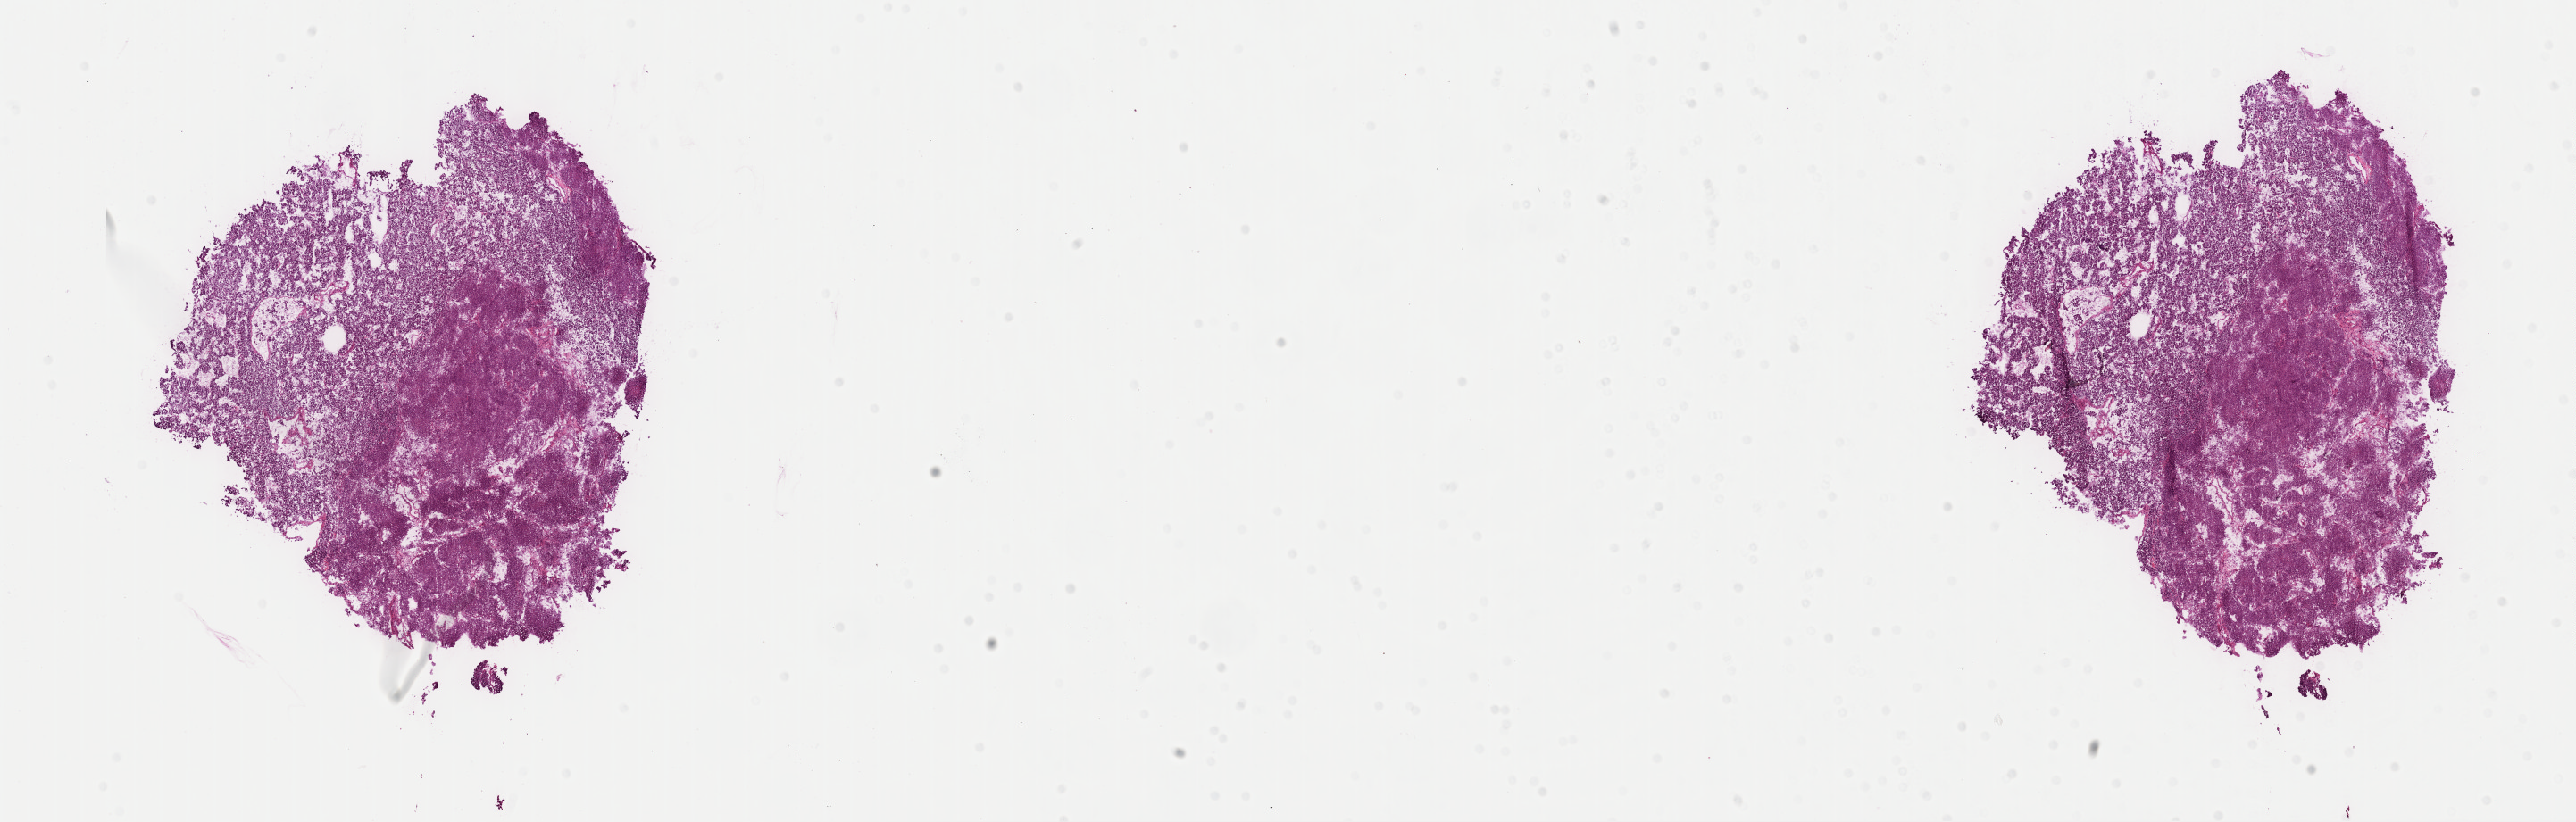
Digitized Hematoxylin and eosin (H&E) stained tissue section (whole slide), low-resolution overview of the scanned area, about 22.8 x 7.3 mm (from a 40x scan). Frozen section from the top of the tissue portion. Primary tumour sample from the adrenal gland. Female patient; age at initial diagnosis 44 years. Slide review estimates, as recorded: tumour cells 85%, tumour nuclei 85%, normal cells 0%, stromal cells 15%, necrosis 0%. Infiltration values recorded for this section: lymphocyte infiltration 0%, monocyte infiltration 0%, neutrophil infiltration 0%.
Laterality: right. Diagnosis: Pheochromocytoma, NOS.